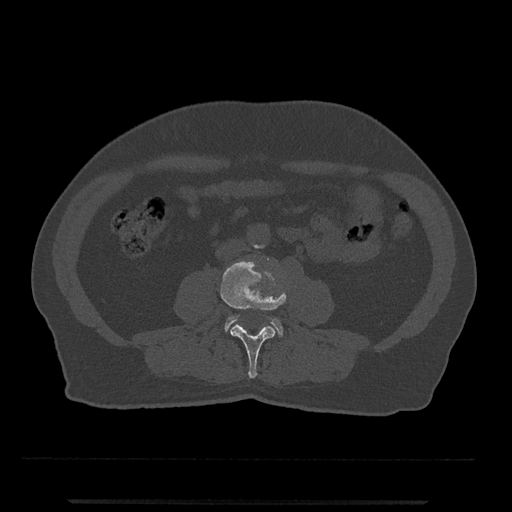
CT including the spine, one axial slice. Position 182 of 797 along the scan axis. Reconstruction kernel Br40s/3. 120 kVp. Bone window (W 1800 / L 400 HU). 512 × 512 image matrix. Patient: male, 63 years. From the clinical record (not read from this slice): primary cancer: prostate.
Structures marked on this image (semi-automatically segmented with operator editing):
- L3 vertebra: box from (x=220, y=260) to (x=287, y=379) px
- L4 vertebra: (x=225, y=316)–(x=284, y=336)